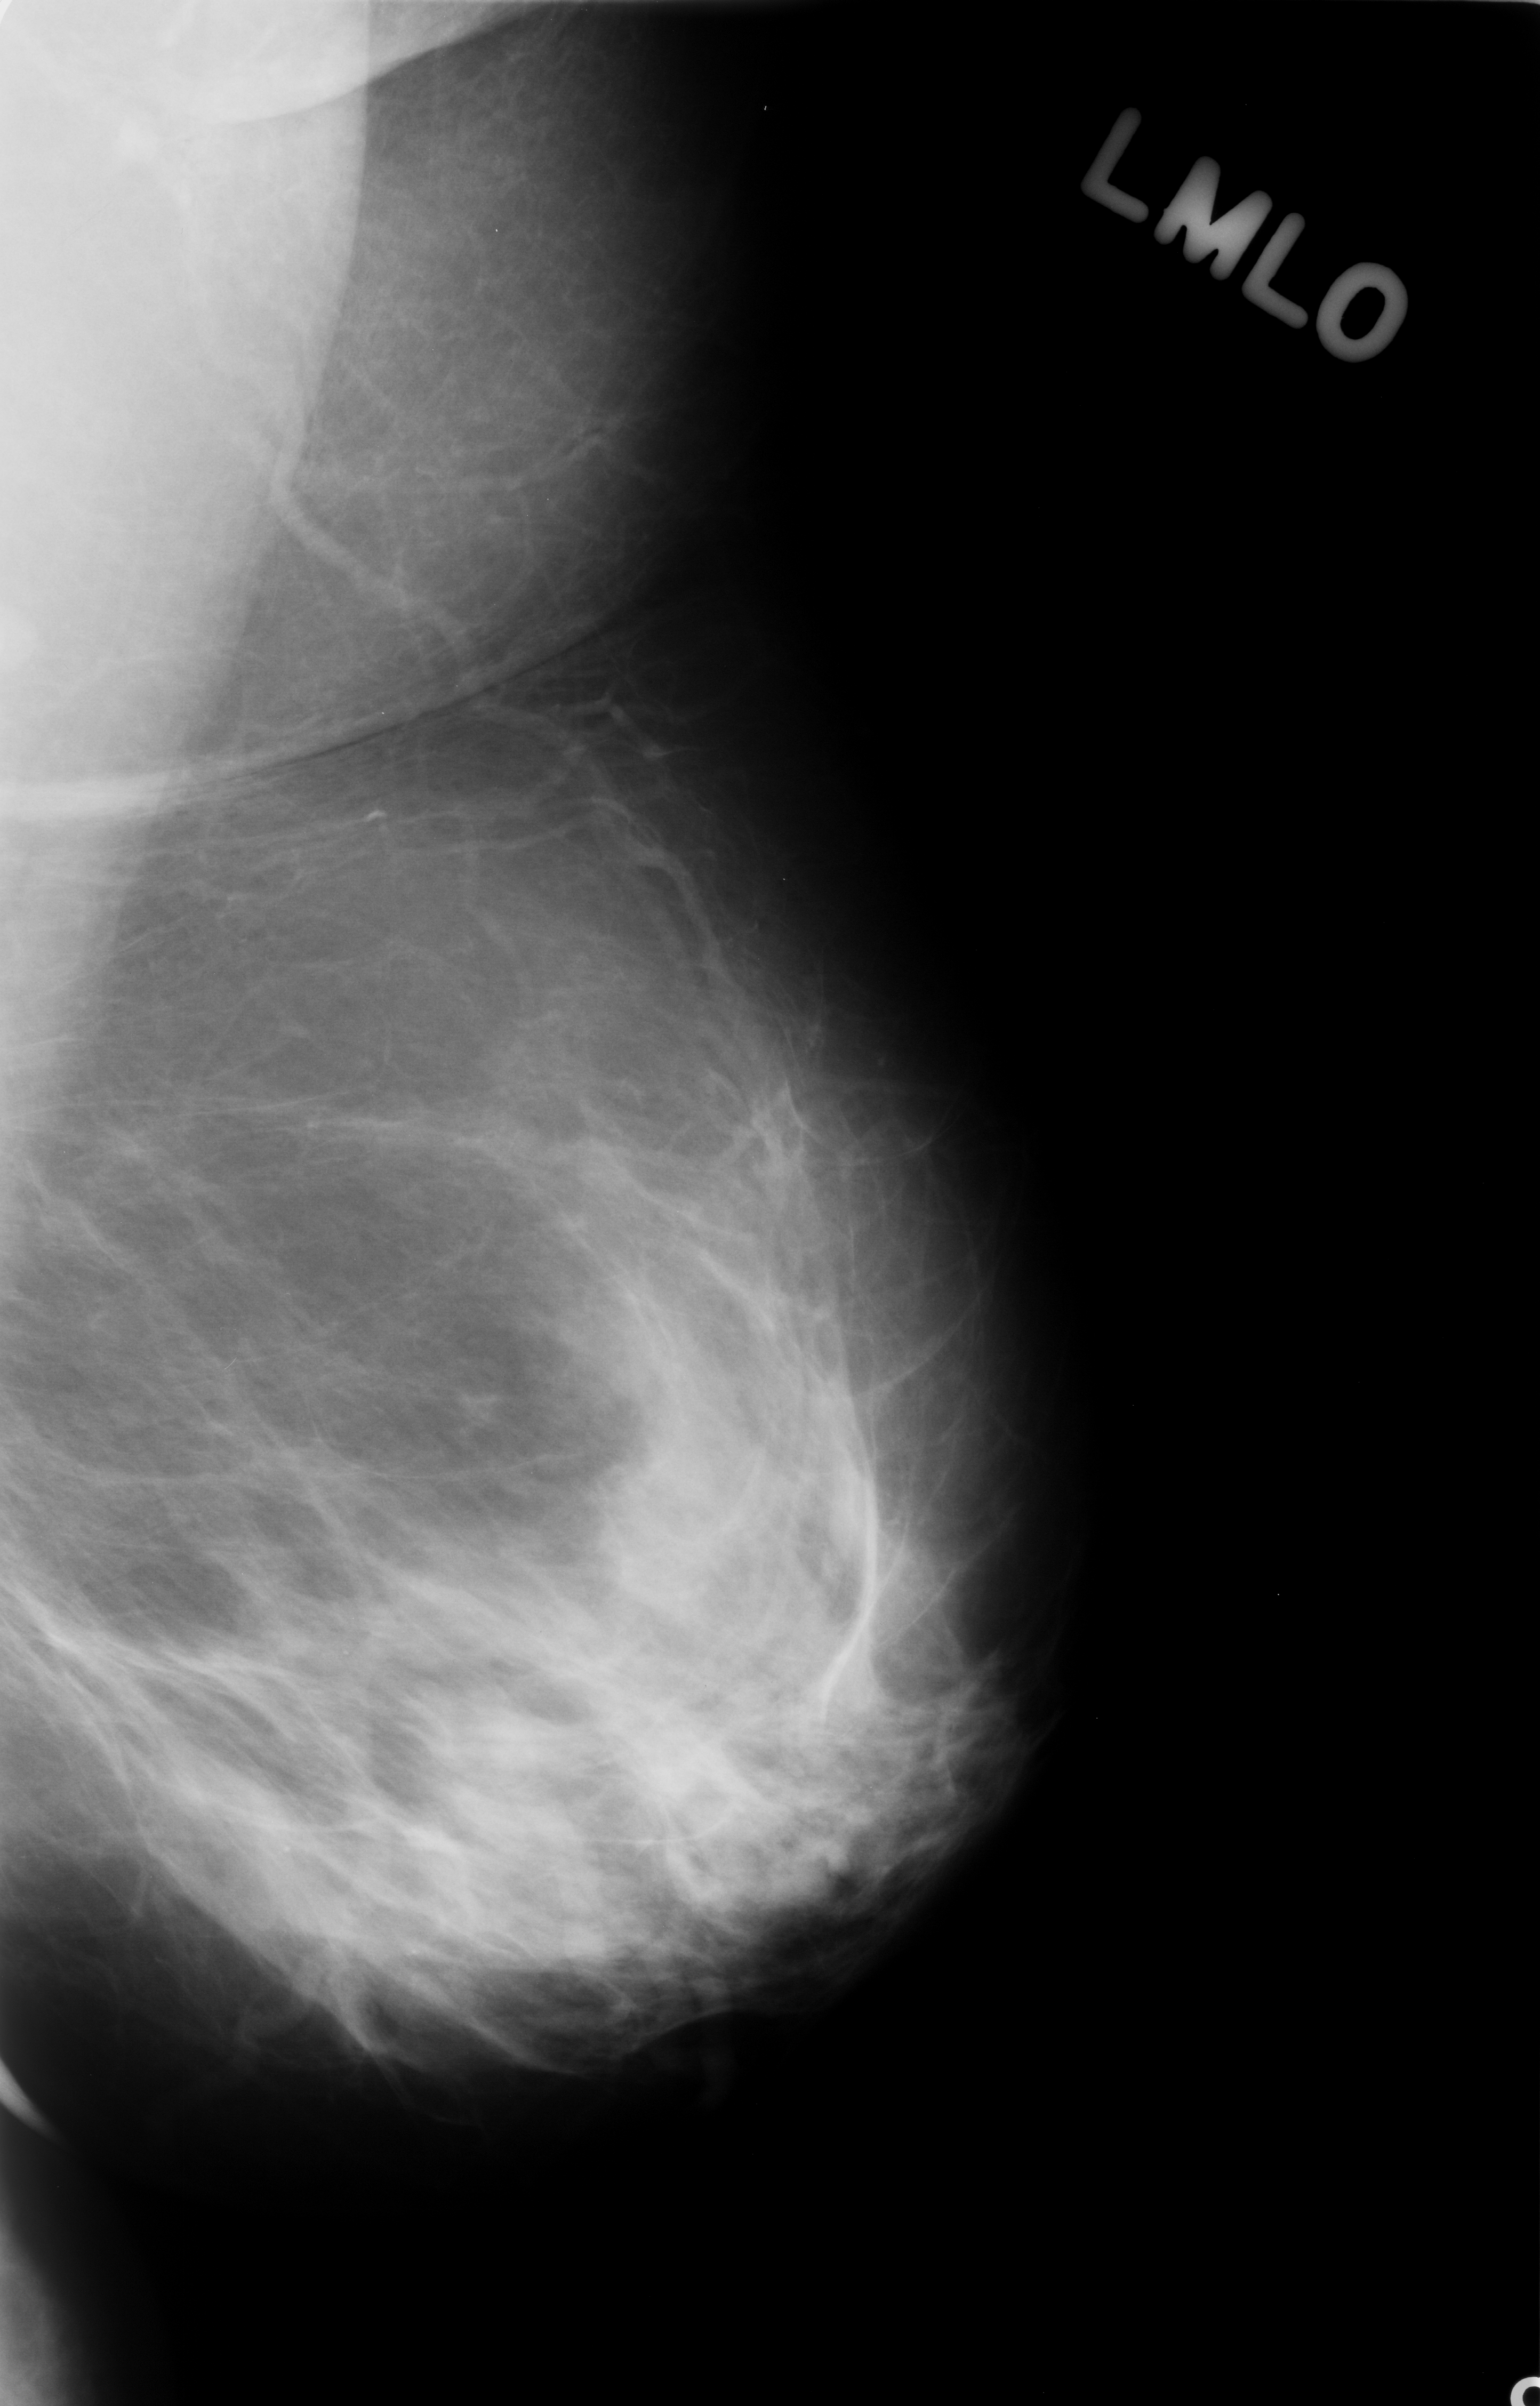
Digitized screen-film mammogram. Left breast. Mediolateral oblique (MLO) view. BI-RADS breast density category 2 (scale 1–4). 1540 × 2406 image matrix.
Expert-marked regions of interest on this image (one box per marked abnormality):
- calcifications, morphology amorphous, distribution segmental; BI-RADS assessment category 4; pathology (as recorded): benign: bounding box (x1, y1, x2, y2) in pixels: (166, 1599, 654, 2036)